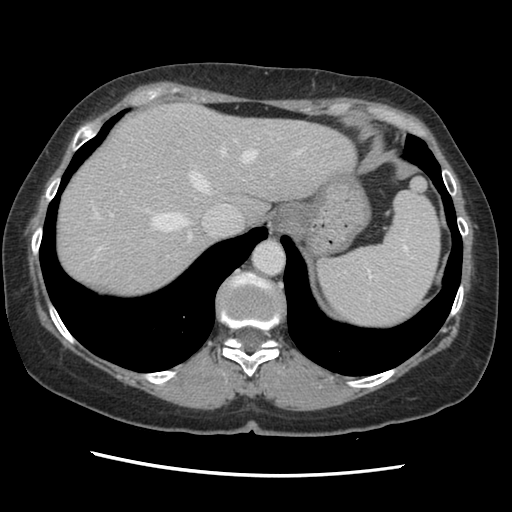
Contrast-enhanced abdominal CT, one axial slice; position 110 of 141 along the scan axis; 120 kVp; soft-tissue window (W 400 / L 40 HU); 2.5 mm slice thickness; 512 × 512 image matrix, field of view 330 × 330 mm. Female patient, age 61 years. From the clinical record (not read from this slice): diagnosis: colorectal cancer liver metastases, imaged before liver resection; multiple liver metastases: no; largest metastasis: 2.4 cm.
Structures marked on this image (expert manual segmentation):
- hepatic veins: bounding box <93,140,303,252> (left, top, right, bottom; pixels)
- liver: <56,104,354,300>
- planned liver remnant (the part of the liver to remain after resection): <56,105,355,300>
- portal vein (with intrahepatic branches): <110,213,168,257>